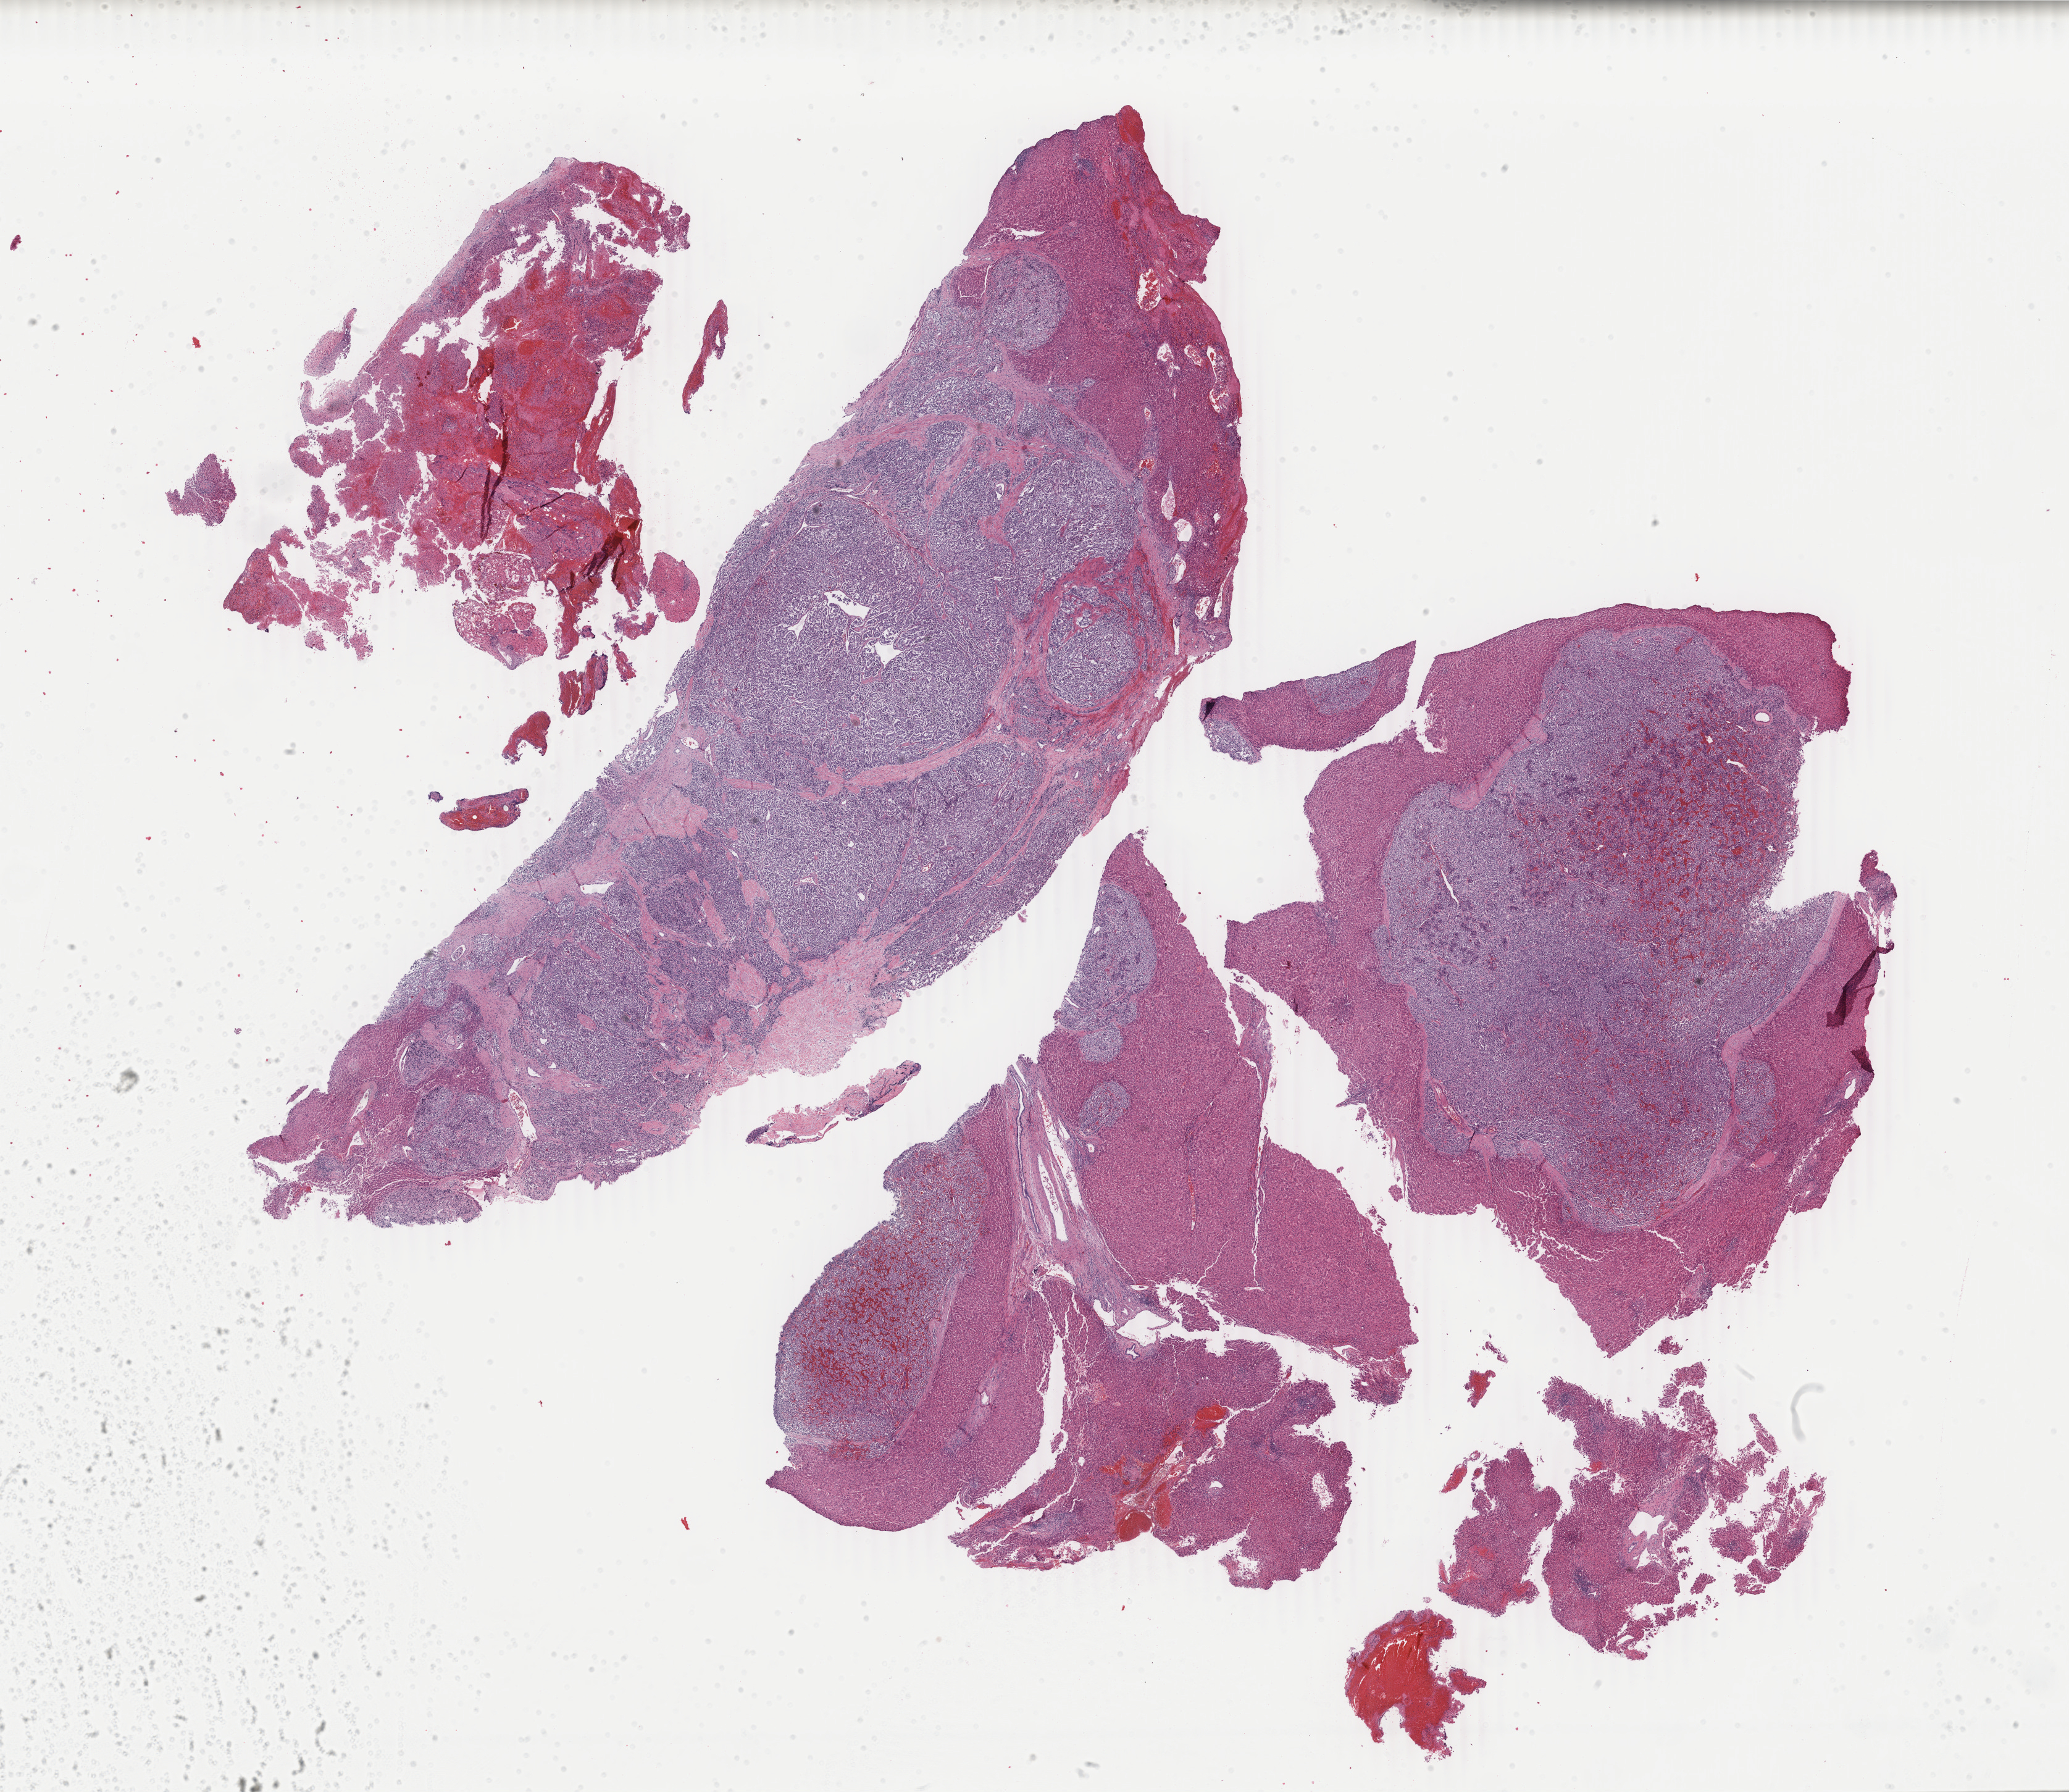
H&E-stained whole-slide image, low-resolution overview of the scanned area, about 26.7 x 23.1 mm (slide scanned at 40x), formalin-fixed paraffin-embedded (FFPE) diagnostic section, additional new primary tumour sample from the spinal cord, cranial nerves, and other parts of central nervous system. Patient: male, age at initial diagnosis 55 years.
This section: additional new primary tumour. Patient diagnosis: Paraganglioma, malignant (nervous system, NOS).